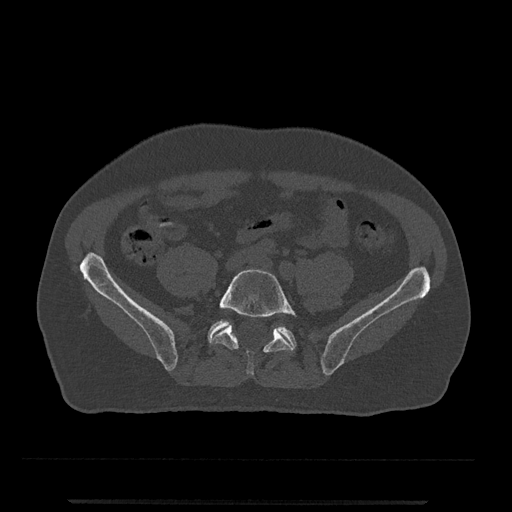
CT including the spine, one axial slice. Slice 62 of 797 in the series (ordered by position). Reconstruction kernel Br40s/3. Bone window (W 1800 / L 400 HU). 0.5 mm slice thickness. 512 × 512 image matrix, field of view 419 × 419 mm. Patient: male, 63 years. From the clinical record (not read from this slice): primary cancer: prostate.
Annotated regions visible in this slice (semi-automatically segmented with operator editing):
- L5 vertebra: box from (x=211, y=268) to (x=297, y=375) px